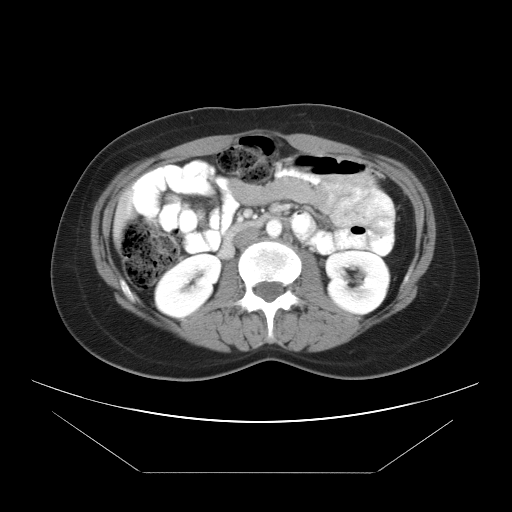
Contrast-enhanced abdominal CT, one axial slice; position 15 of 34 along the scan axis; soft-tissue window (W 400 / L 40 HU); 7.5 mm slice thickness; 512 × 512 image matrix. Female patient, age 38 years. Case-level facts recorded for this patient, not image findings: diagnosis: colorectal cancer liver metastases, imaged before liver resection; multiple liver metastases: yes; largest metastasis: 3.1 cm; disease in both lobes: no.
Outlined on this slice (expert manual segmentation):
- liver: box from (x=115, y=193) to (x=132, y=225) px